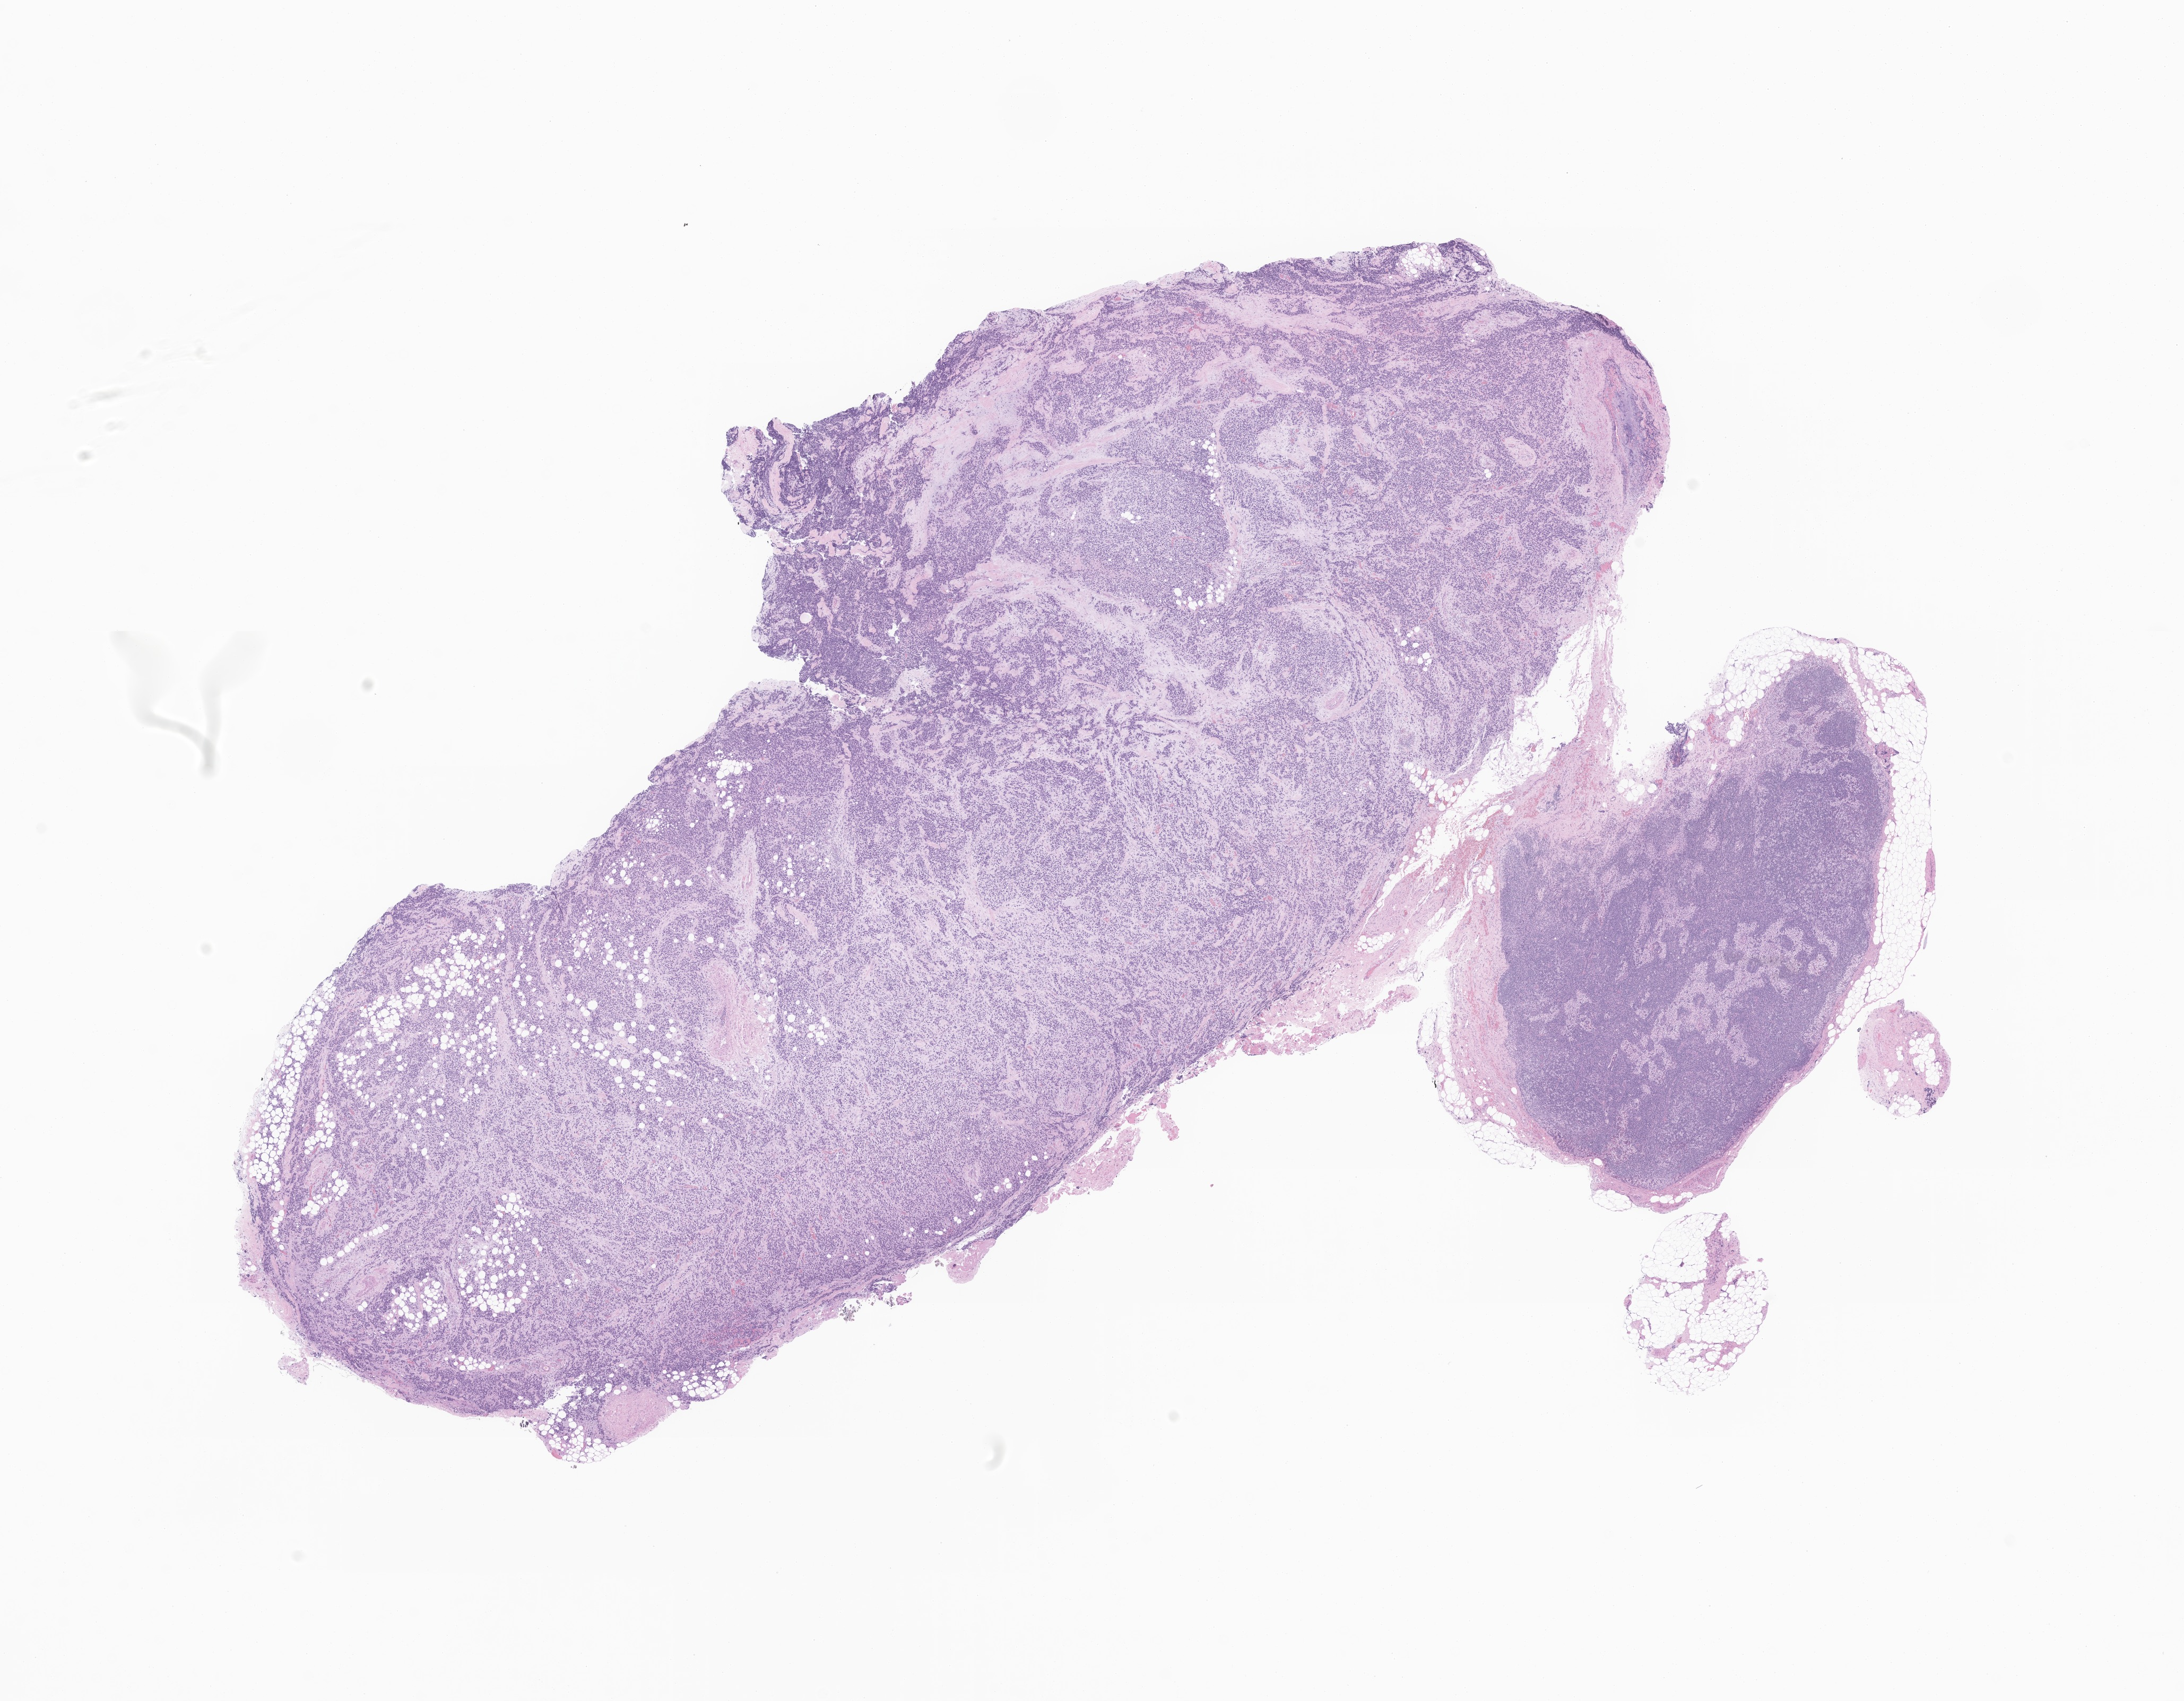
Whole-slide image, H&E stain of tumor tissue from the lower limb, low-resolution overview of the scanned area, about 17.4 x 13.5 mm, FFPE section. Patient female; age 241 months (20 years 1 month).
• diagnosis (ICD-O-3 morphology term): Alveolar rhabdomyosarcoma